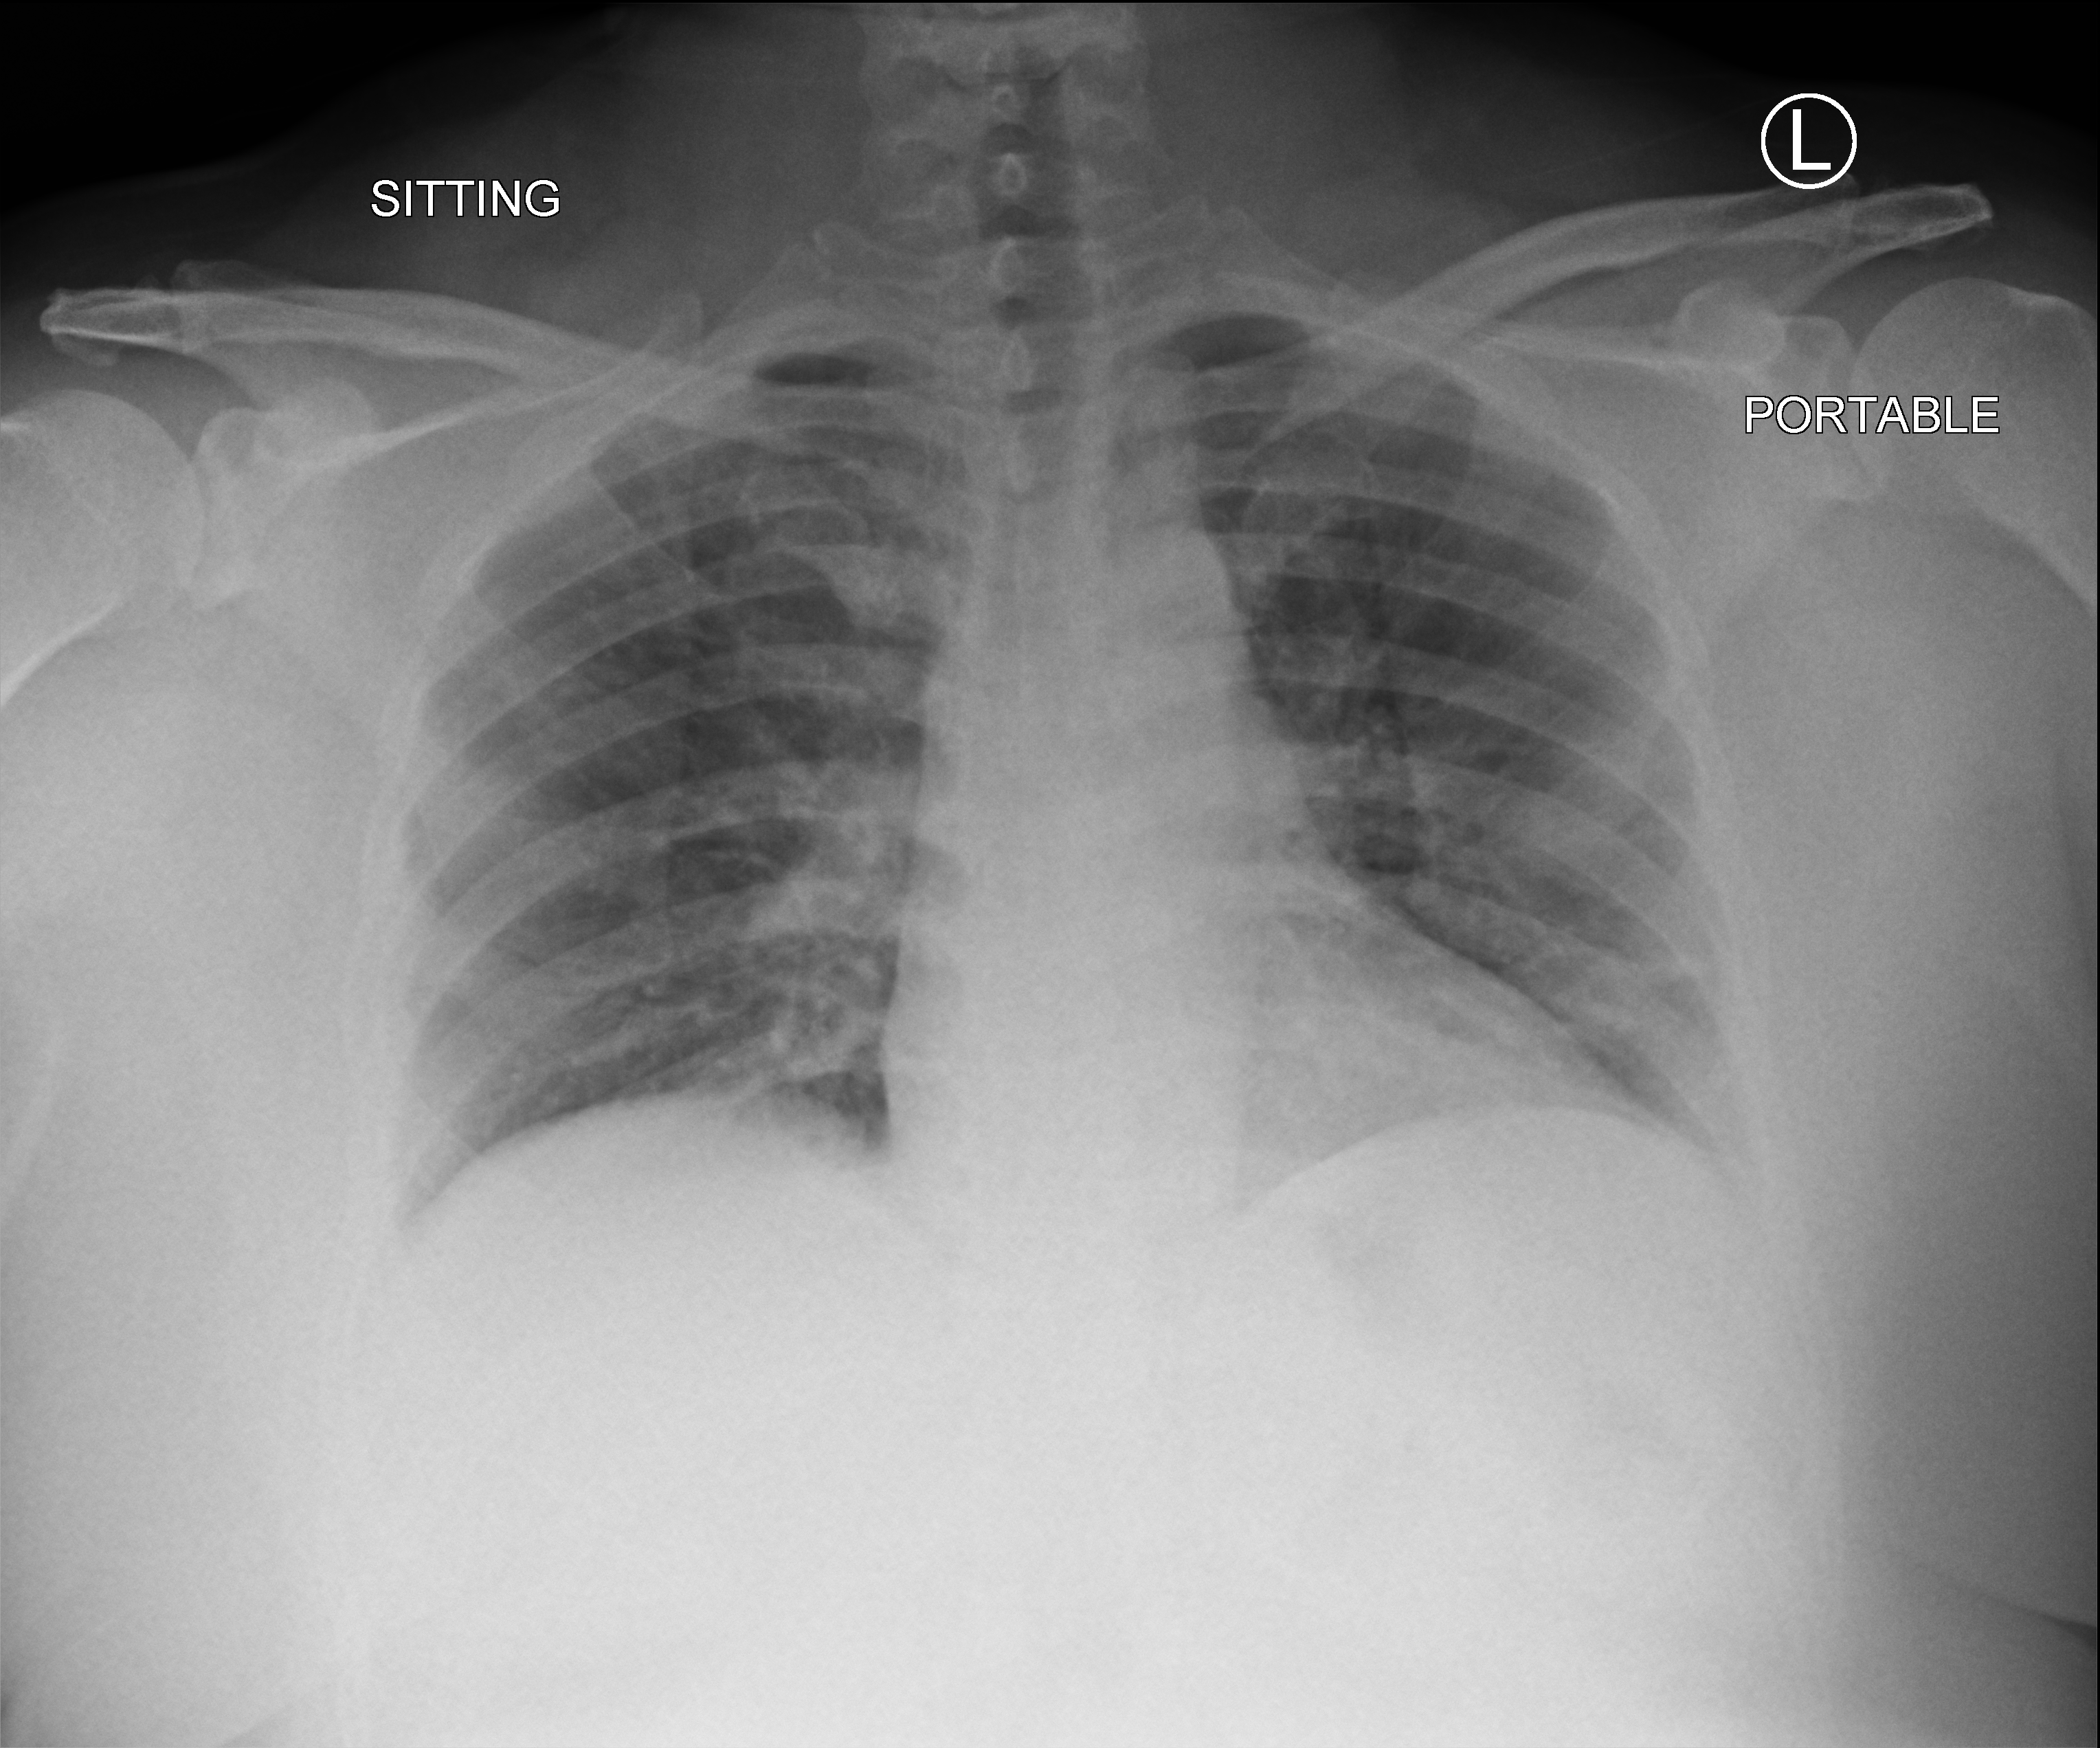
Bedside chest radiograph (computed radiography); anteroposterior (AP) projection. Male patient hospitalised with COVID-19, age 18–59 years.
From the hospital-stay record, not from the radiograph (when in the stay this image was taken is not recorded): mechanically ventilated during this hospital stay: no; admitted to intensive care during this hospital stay: no; COPD (admission record): no.